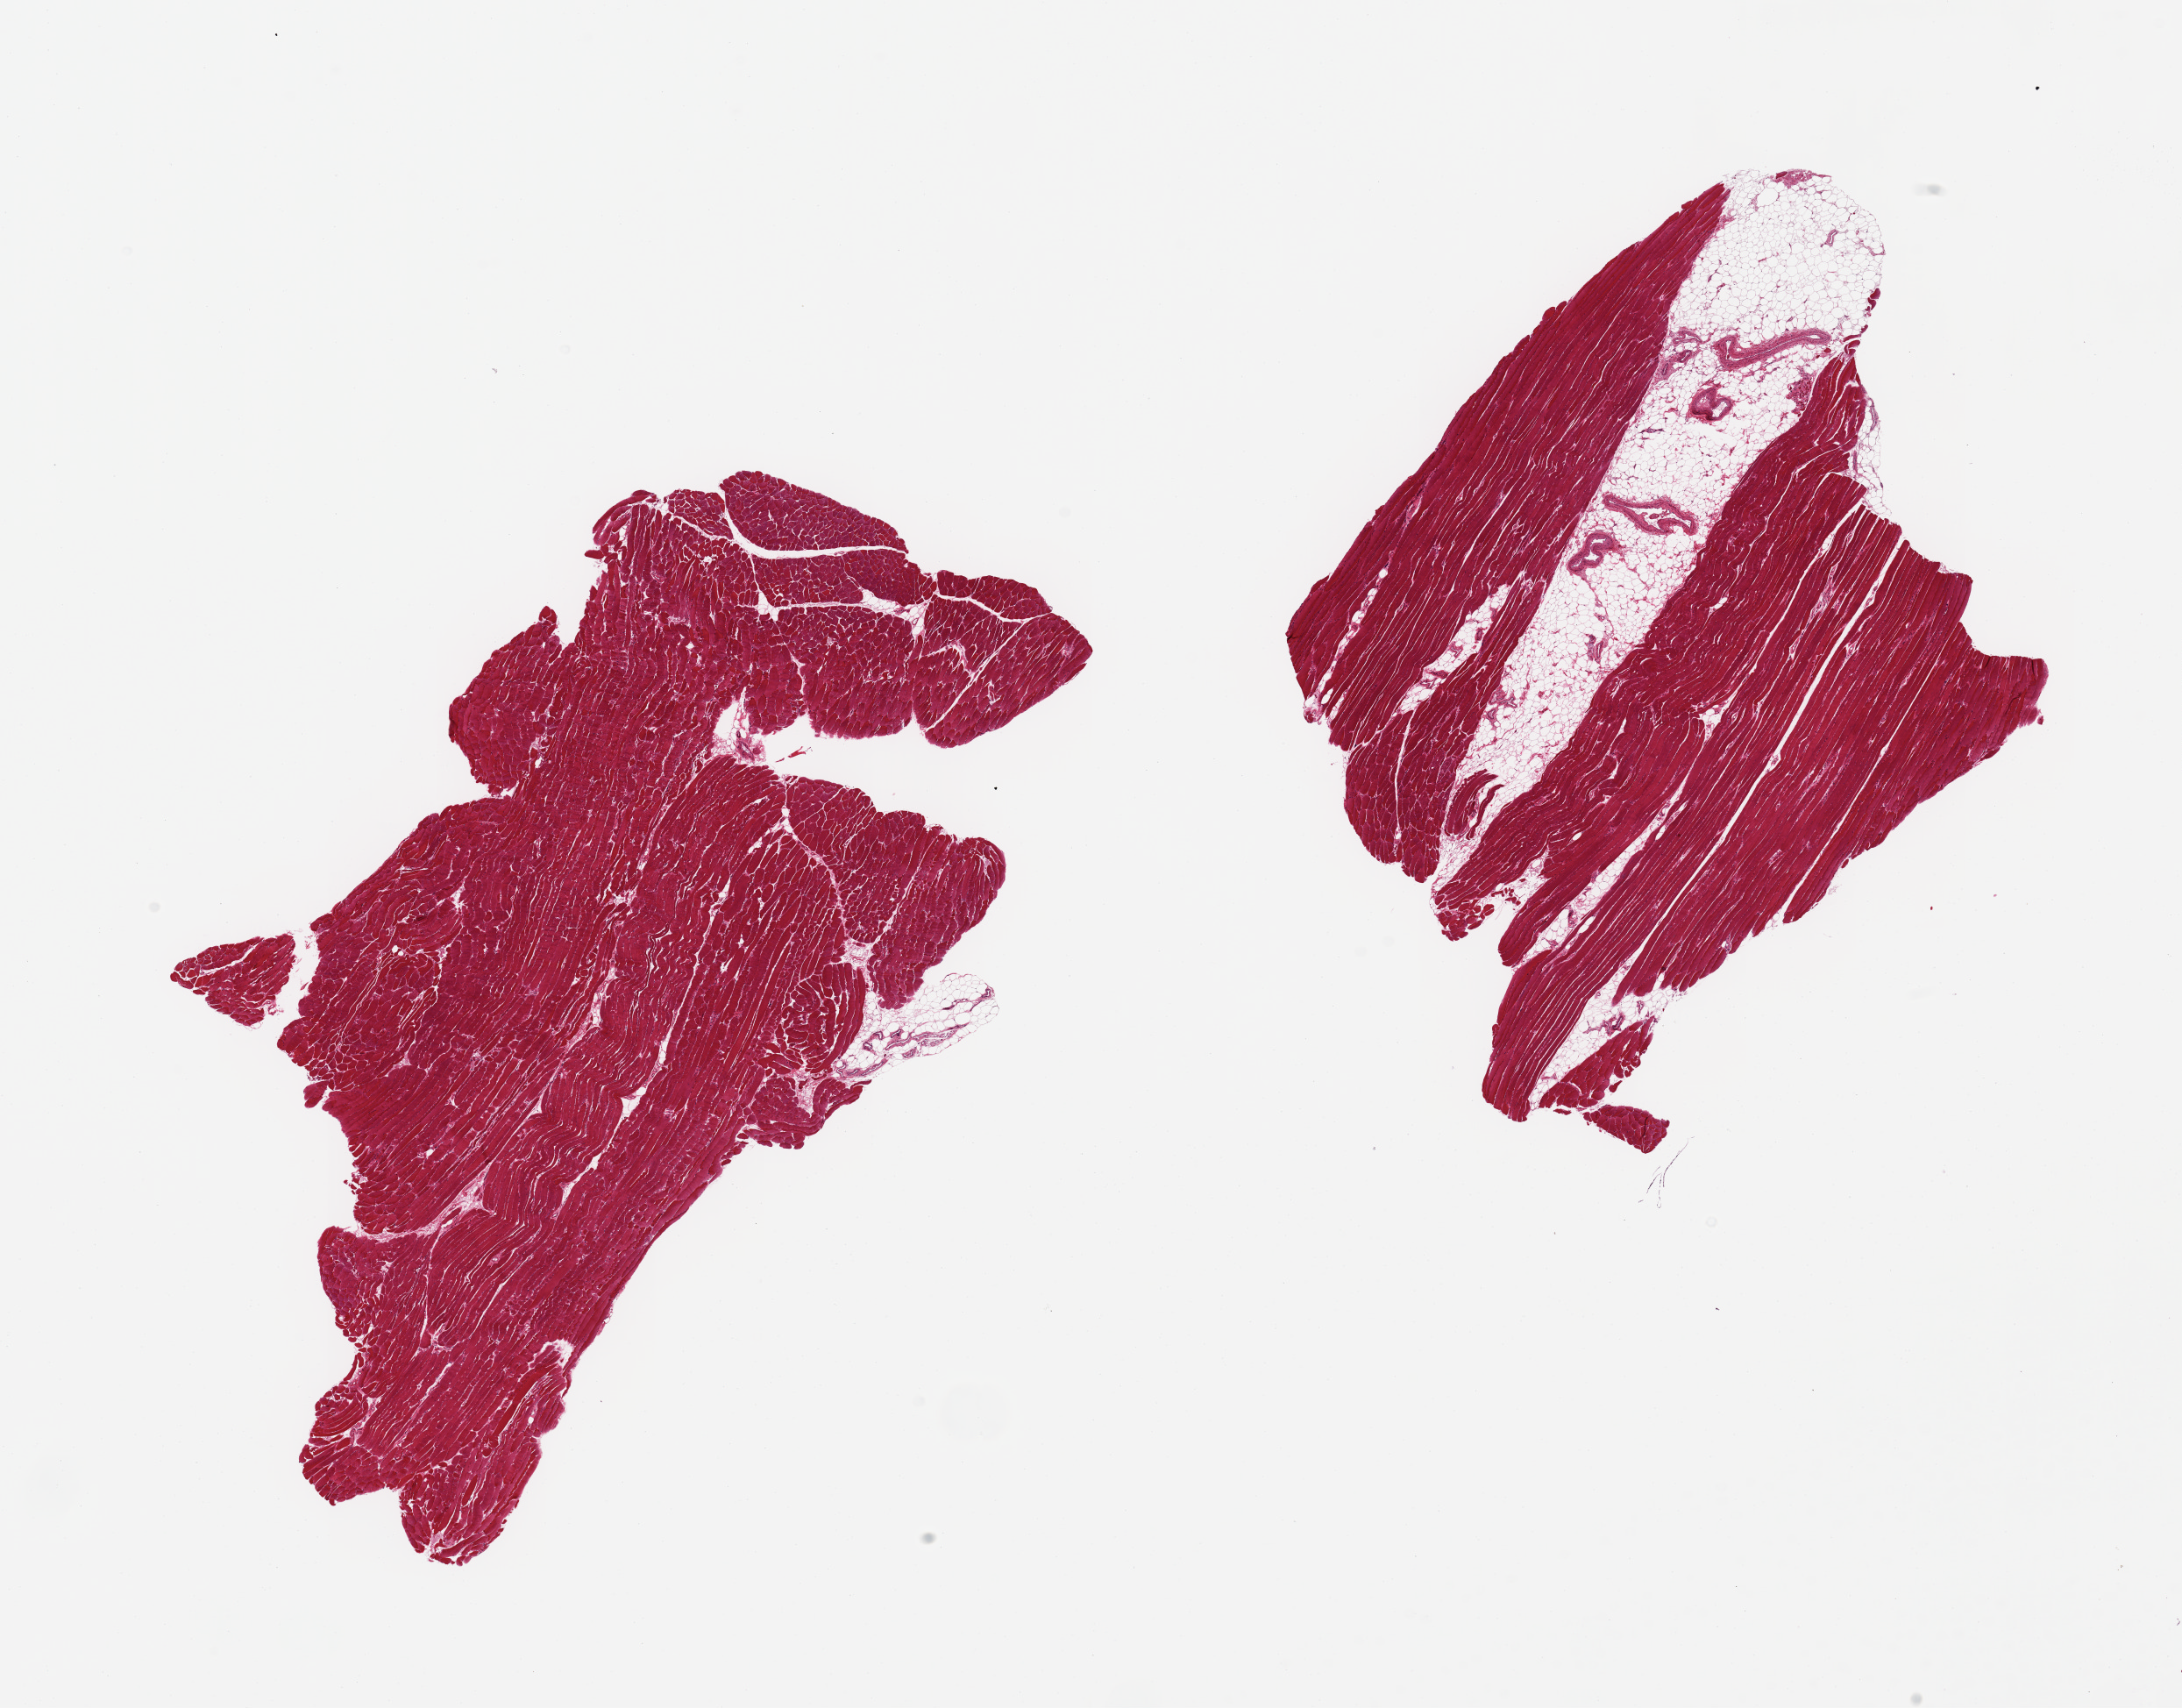
Digitized haematoxylin and eosin-stained section, whole scanned area (about 19.7 x 15.4 mm, slide scanned at 20x) shown as a low-resolution overview. PAXgene-fixed paraffin-embedded (PFPE) section. Section of skeletal muscle (target tissue). Tissue donor sample. Donor sex: male.
Pathologist's review note for this sample: 2 pieces, 1 with 20% internal fat; scattered atrophy.